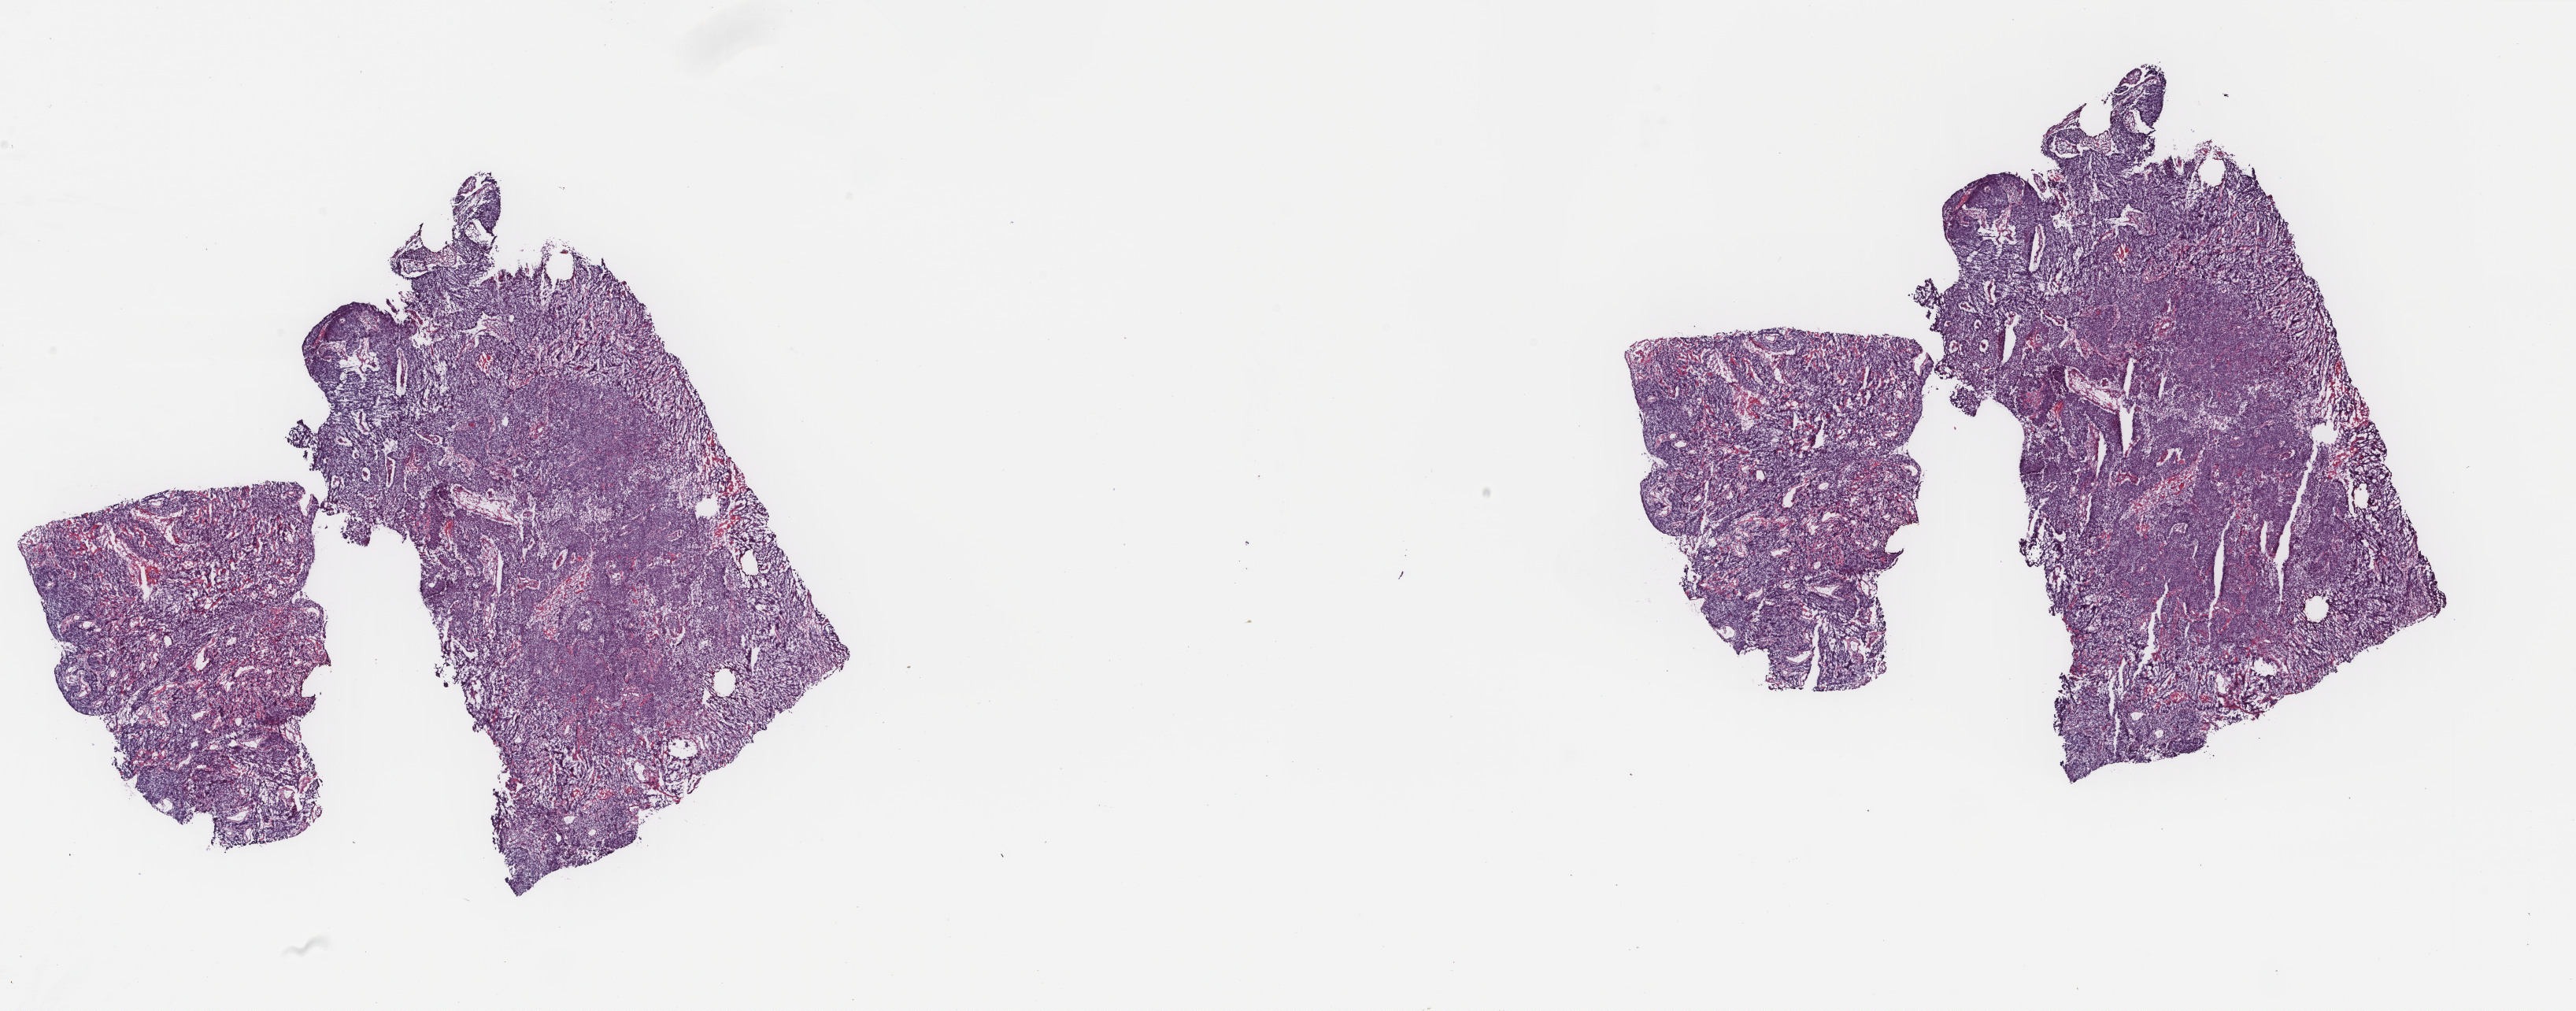
Digitized H&E-stained tissue section (whole slide), a low-resolution overview of the entire scanned area, about 26.0 x 10.2 mm, frozen section, cervix, primary tumour sample. Patient: female, age at initial diagnosis 78 years. Histologic grade: G3 (poorly differentiated). Composition of this section per pathologist review: tumour cells 70%, tumour nuclei 70%, normal cells 0%, stromal cells 25%, necrosis 5%. Infiltration values recorded for this section: lymphocyte infiltration 60%, monocyte infiltration 10%, neutrophil infiltration 10%.
* FIGO stage: IB2
* lymph nodes positive (case pathology): 0 of 30 examined
* diagnosis: Squamous cell carcinoma, NOS (cervix uteri)